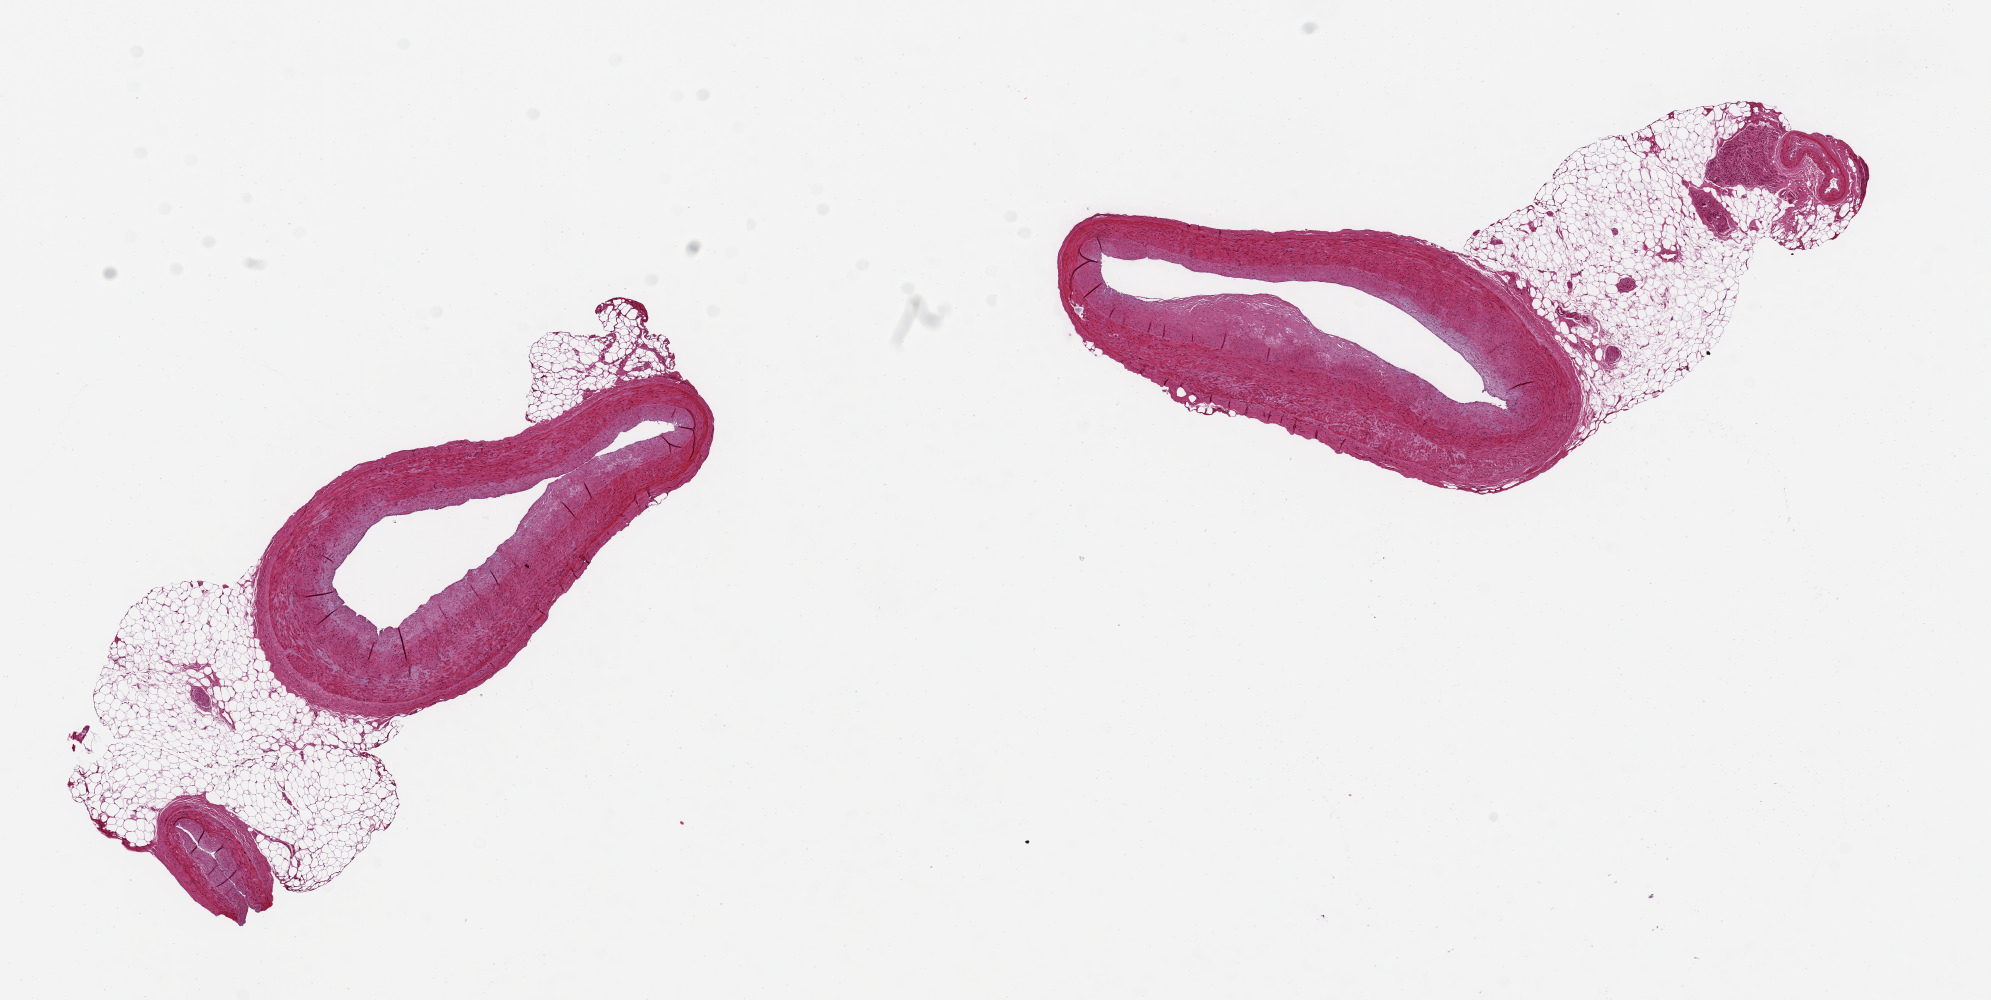
Haematoxylin and eosin whole-slide image, shown as a low-resolution overview of the whole scanned area (about 15.8 x 7.9 mm, from a 20x scan). PAXgene-fixed, paraffin-embedded tissue. Sampled site (target tissue): coronary artery. Donor tissue sample.
• review note (as recorded): pieces 4x2 mm arteries with a 3x2 mm adherent adipose attachment; eccentric plaque